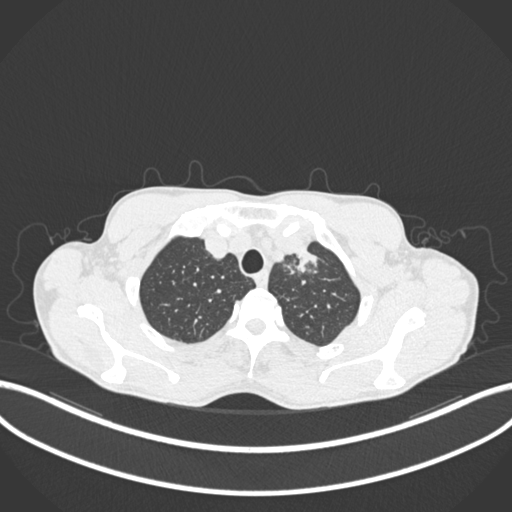
Chest CT, one axial slice; slice 178 of 211 in the series (ordered by position); reconstruction kernel B30f; lung window (W 1500 / L -600 HU); 1 mm slice thickness; 512 × 512 image matrix. Patient: male, 58 years. From the clinical record (not read from this slice): clinical TNM (as recorded): T1c N1 M0.
Structures marked on this image (bounding box drawn by a radiologist):
- lung tumour (recorded histology: adenocarcinoma): bounding box <289,241,323,281> (left, top, right, bottom; pixels)